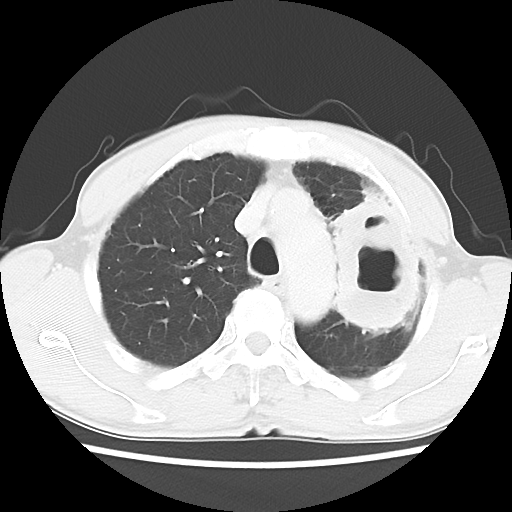
Chest CT, one axial slice; slice 45 of 60 in the series (ordered by position); reconstruction kernel LUNG; lung window (W 1500 / L -600 HU); 5 mm slice thickness; 512 × 512 image matrix, field of view 308 × 308 mm. Male patient, age 64 years. From the clinical record (not read from this slice): clinical TNM (as recorded): T3 N3 M0; histopathological grade: G3.
Structures marked on this image (rectangle marked by the reading radiologist):
- lung tumour (recorded histology: adenocarcinoma): bounding box <312,183,427,342> (left, top, right, bottom; pixels)